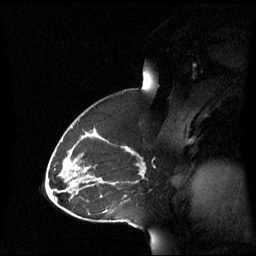
Breast MRI (dynamic contrast-enhanced), one sagittal slice. Slice 38 of 60 in the series (ordered by position). Dynamic contrast-enhanced series, image 2 of 3 at this slice position (ordered by acquisition). 1.5 T. TE 4.2 ms, TR 8.4 ms. 256 × 256 image matrix, field of view 270 × 270 mm. Patient: female, 43 years. From the clinical record (not read from this slice): setting: breast cancer imaged before/during neoadjuvant chemotherapy; receptor status: triple-negative.
Annotated regions visible in this slice (semi-automatically segmented with operator editing):
- analysis volume of interest (the breast-tissue region the enhancement analysis was run in; not a lesion): box from (x=69, y=137) to (x=143, y=198) px
- tumour enhancement mask (voxels above the 70 % enhancement threshold inside the analysis volume of interest): (x=124, y=147)–(x=143, y=196)